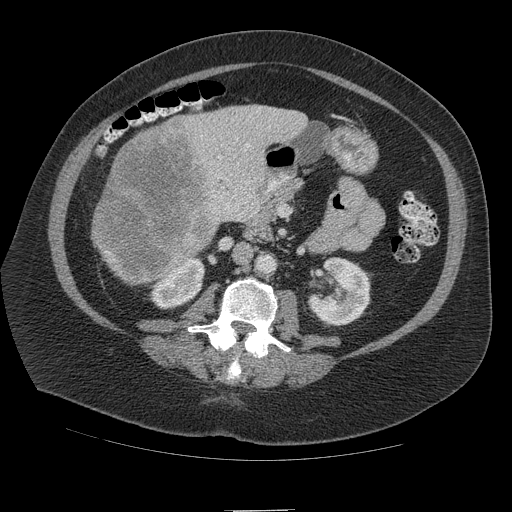
Contrast-enhanced abdominal CT (liver protocol), one axial slice. Position 39 of 109 along the scan axis. Reconstruction kernel STANDARD. Soft-tissue window (W 400 / L 40 HU). 512 × 512 image matrix, field of view 420 × 420 mm. From the clinical record (not read from this slice): diagnosis: hepatocellular carcinoma (patient treated with transarterial chemoembolisation; whether this scan precedes or follows treatment is not stated here); TNM stage (as recorded): Stage-IVB; Child-Pugh class: A.
Outlined on this slice (semi-automatically segmented with operator editing):
- liver parenchyma outside the tumour (the mass and vessels are separate outlines, so this box may not span the whole liver): bounding box (x1, y1, x2, y2) in pixels: (94, 104, 308, 284)
- mass: (91, 120, 216, 284)
- liver vessels: (214, 138, 251, 216)